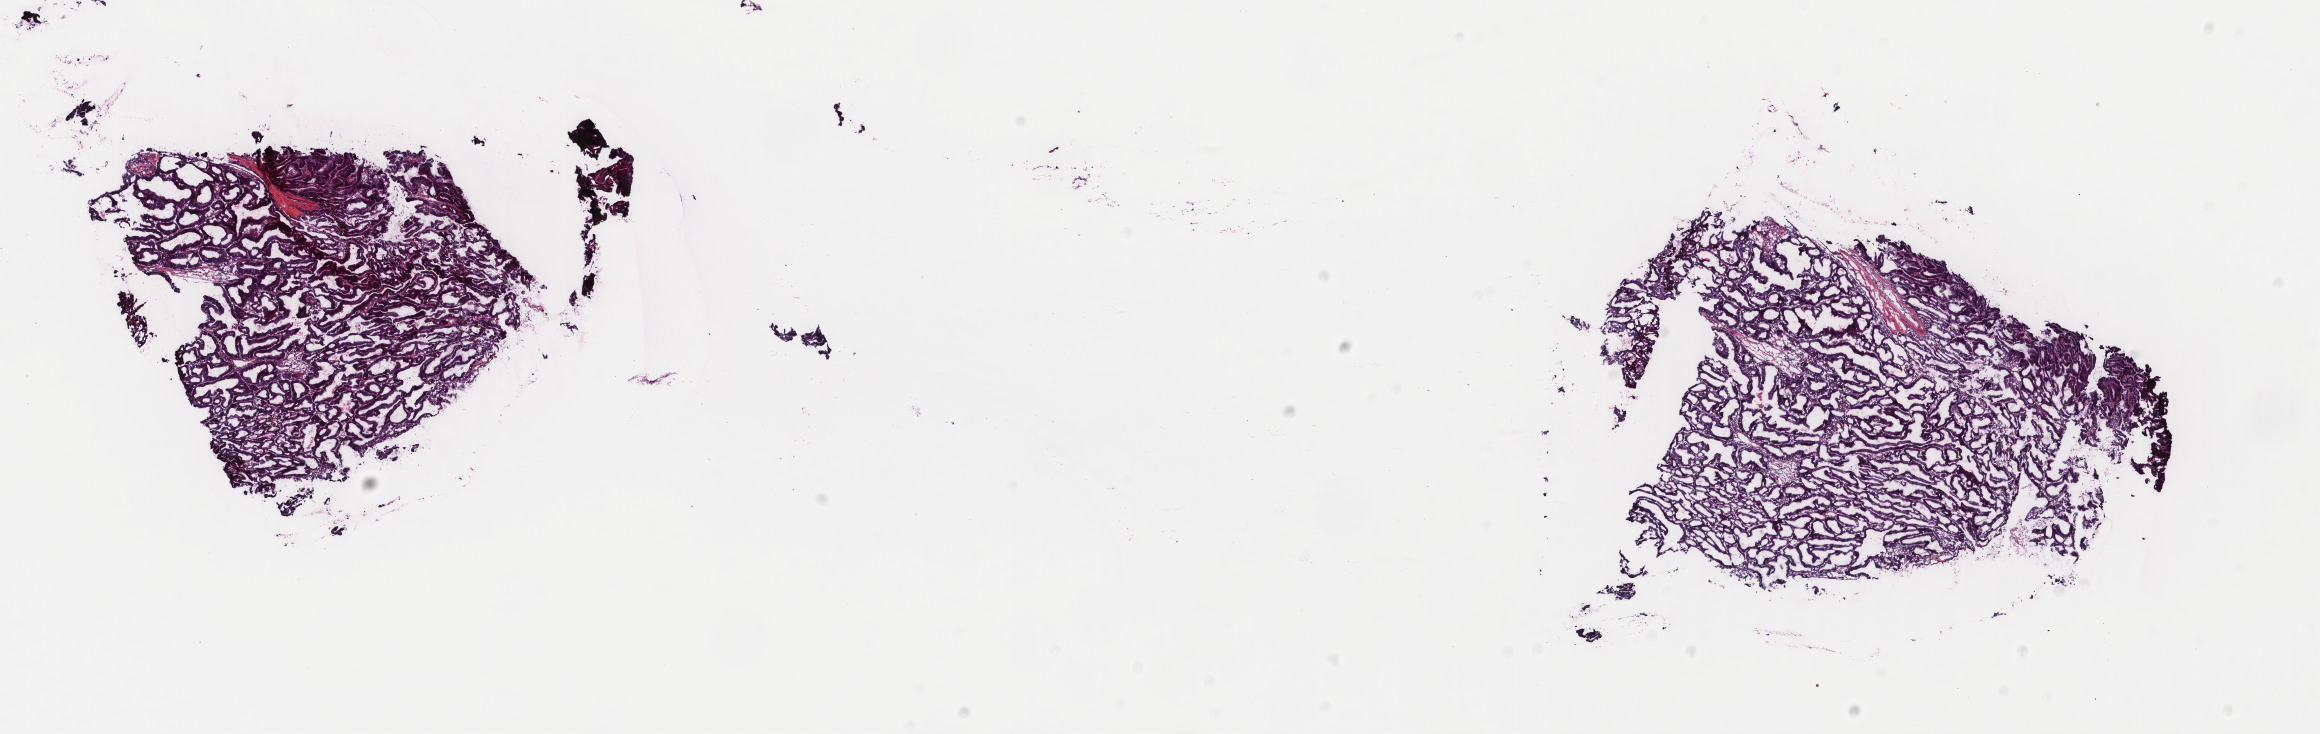
Digitized H&E-stained tissue section (whole slide) — low-resolution overview of the scanned area, about 18.4 x 5.8 mm (acquisition: 40x scan), frozen section, uterus, primary tumour sample. Female patient; age at initial diagnosis 61 years. Histologic grade: G1 (well differentiated). Composition of this section per pathologist review: tumour cells 93%, tumour nuclei 95%, normal cells 3%, stromal cells 3%, necrosis 1%. Infiltration values recorded for this section: lymphocyte infiltration 2%, monocyte infiltration 0%, neutrophil infiltration 0%.
* histologic diagnosis: Endometrioid adenocarcinoma, NOS (endometrium)
* FIGO stage: IB